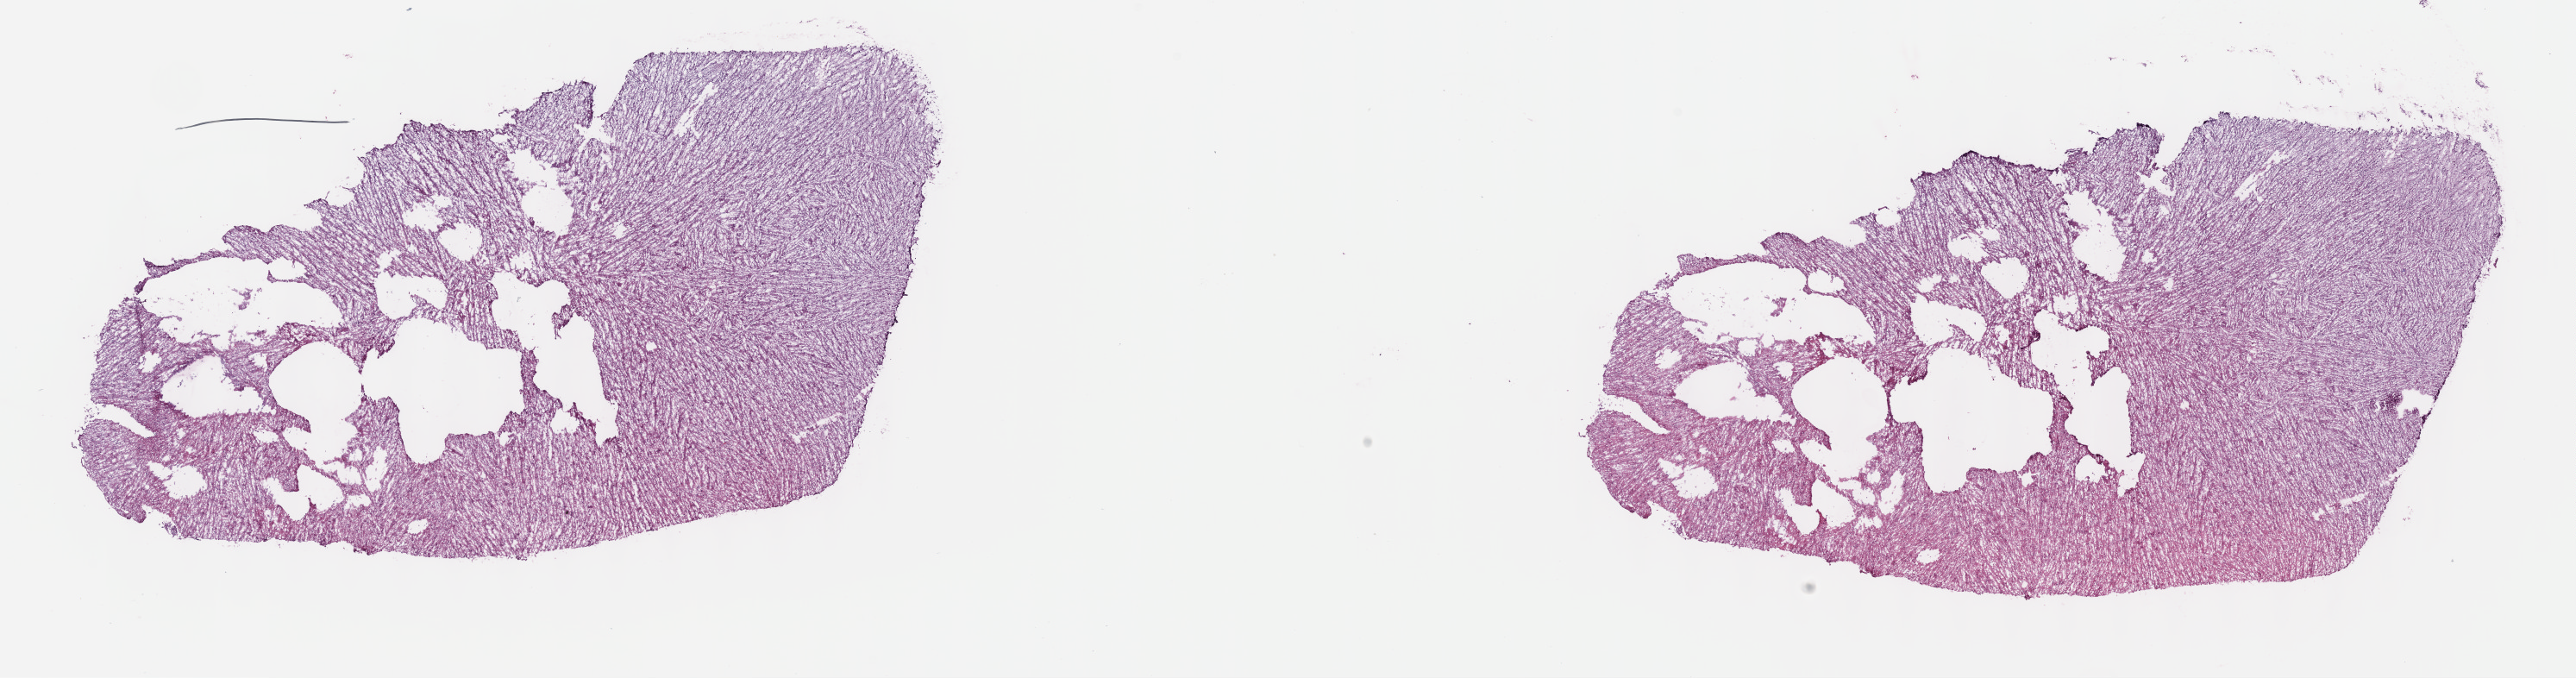
Whole-slide histology image, H&E-stained — whole scanned area (about 24.2 x 6.4 mm, slide scanned at 40x) shown as a low-resolution overview. Frozen section from the top of the tissue portion. Sample: primary tumour, brain. Patient: male, age at initial diagnosis 43 years. Histologic grade: G2 (moderately differentiated). Slide review estimates, as recorded: tumour cells 60%, tumour nuclei 80%, normal cells 10%, stromal cells 30%, necrosis 0%. Infiltration values recorded for this section: lymphocyte infiltration 0%, monocyte infiltration 0%, neutrophil infiltration 0%.
Pathologic diagnosis: Oligodendroglioma, NOS (cerebrum). Laterality: right.